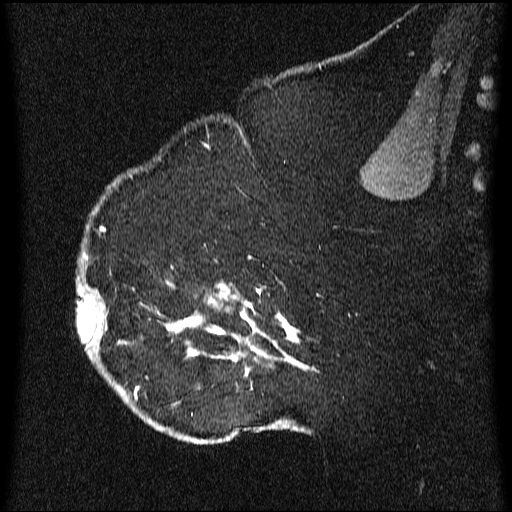
Breast MRI (dynamic contrast-enhanced), one sagittal slice. Dynamic contrast-enhanced series, image 2 of 3 at this slice position (ordered by acquisition). 1.5 T. TE 4.2 ms, TR 9.1 ms. 2.2 mm slice thickness. 512 × 512 image matrix, field of view 180 × 180 mm. Patient: female, 52 years.
Structures marked on this image (semi-automatically segmented with operator editing):
- analysis volume of interest (the breast-tissue region the enhancement analysis was run in; not a lesion): bounding box <76,203,325,438> (left, top, right, bottom; pixels)
- tumour enhancement mask (voxels above the 70 % enhancement threshold inside the analysis volume of interest): <77,228,316,433>